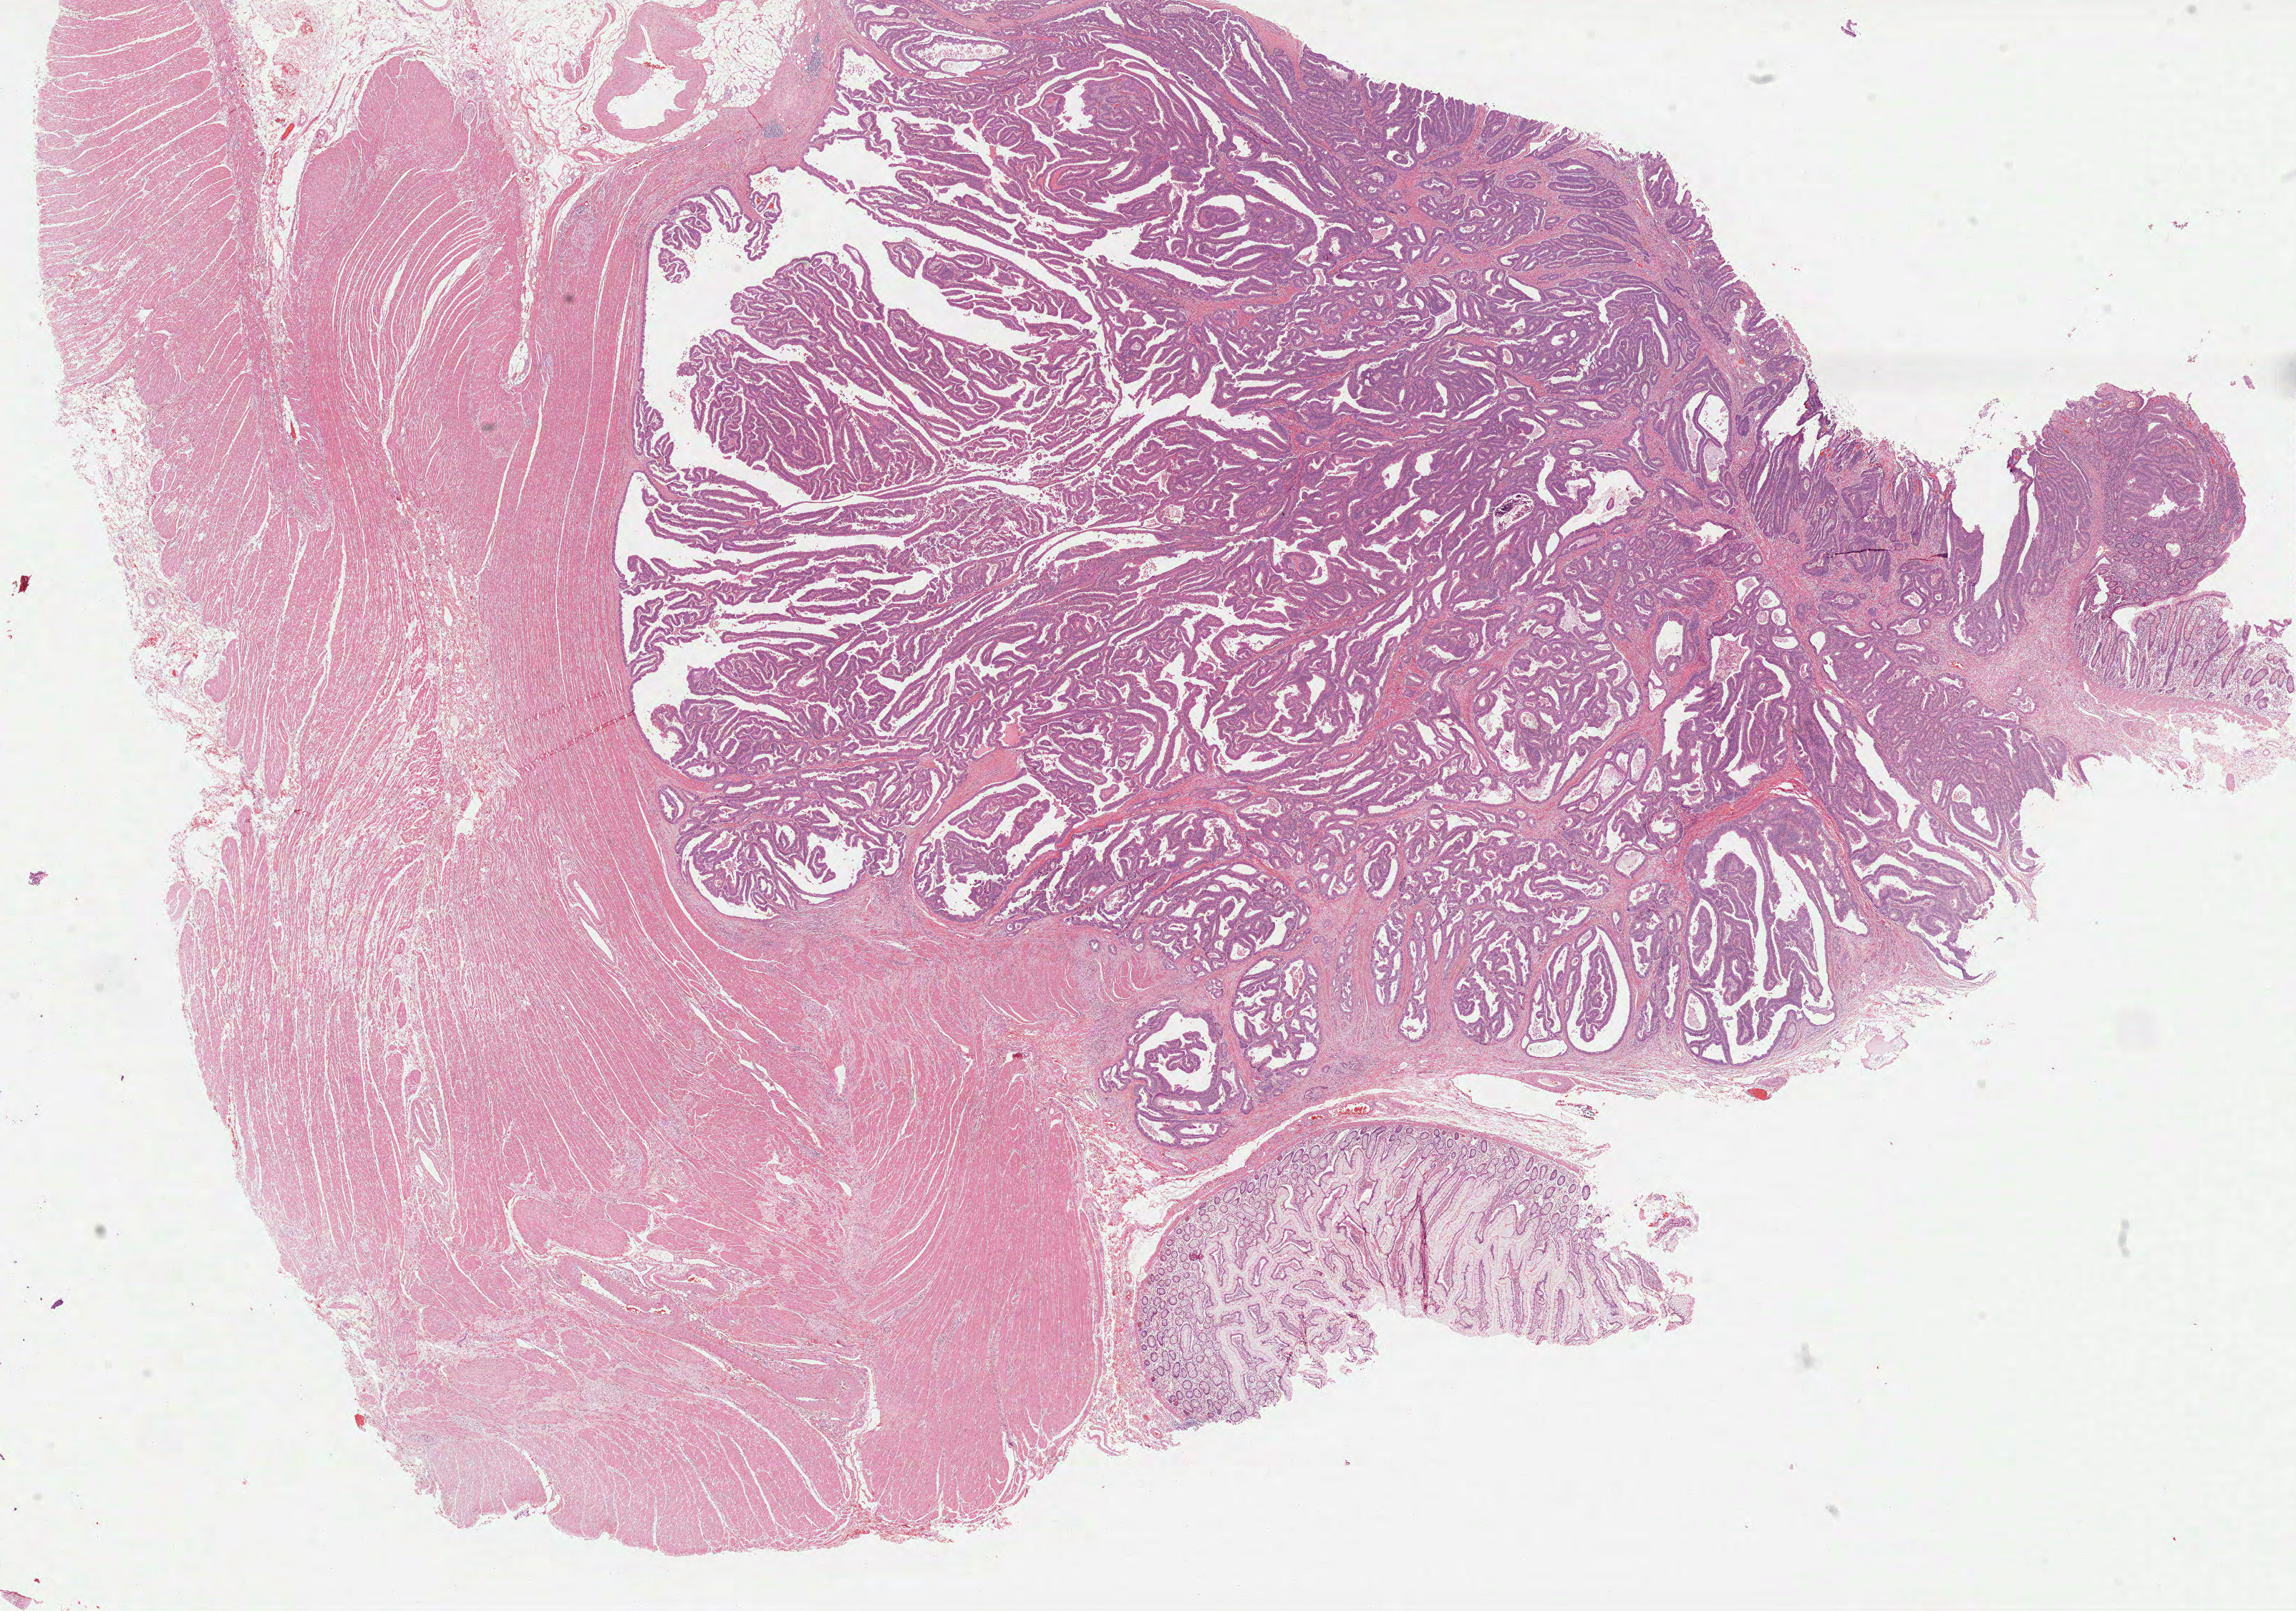
Whole-slide histology image, H&E-stained — shown as a low-resolution overview of the whole scanned area (about 25.9 x 18.1 mm); FFPE section; colon, primary tumour sample. Patient: male, age at initial diagnosis 75 years.
• diagnosis: Adenocarcinoma, NOS
• AJCC pathologic stage: IV
• lymph nodes positive (case pathology): 2 of 10 examined